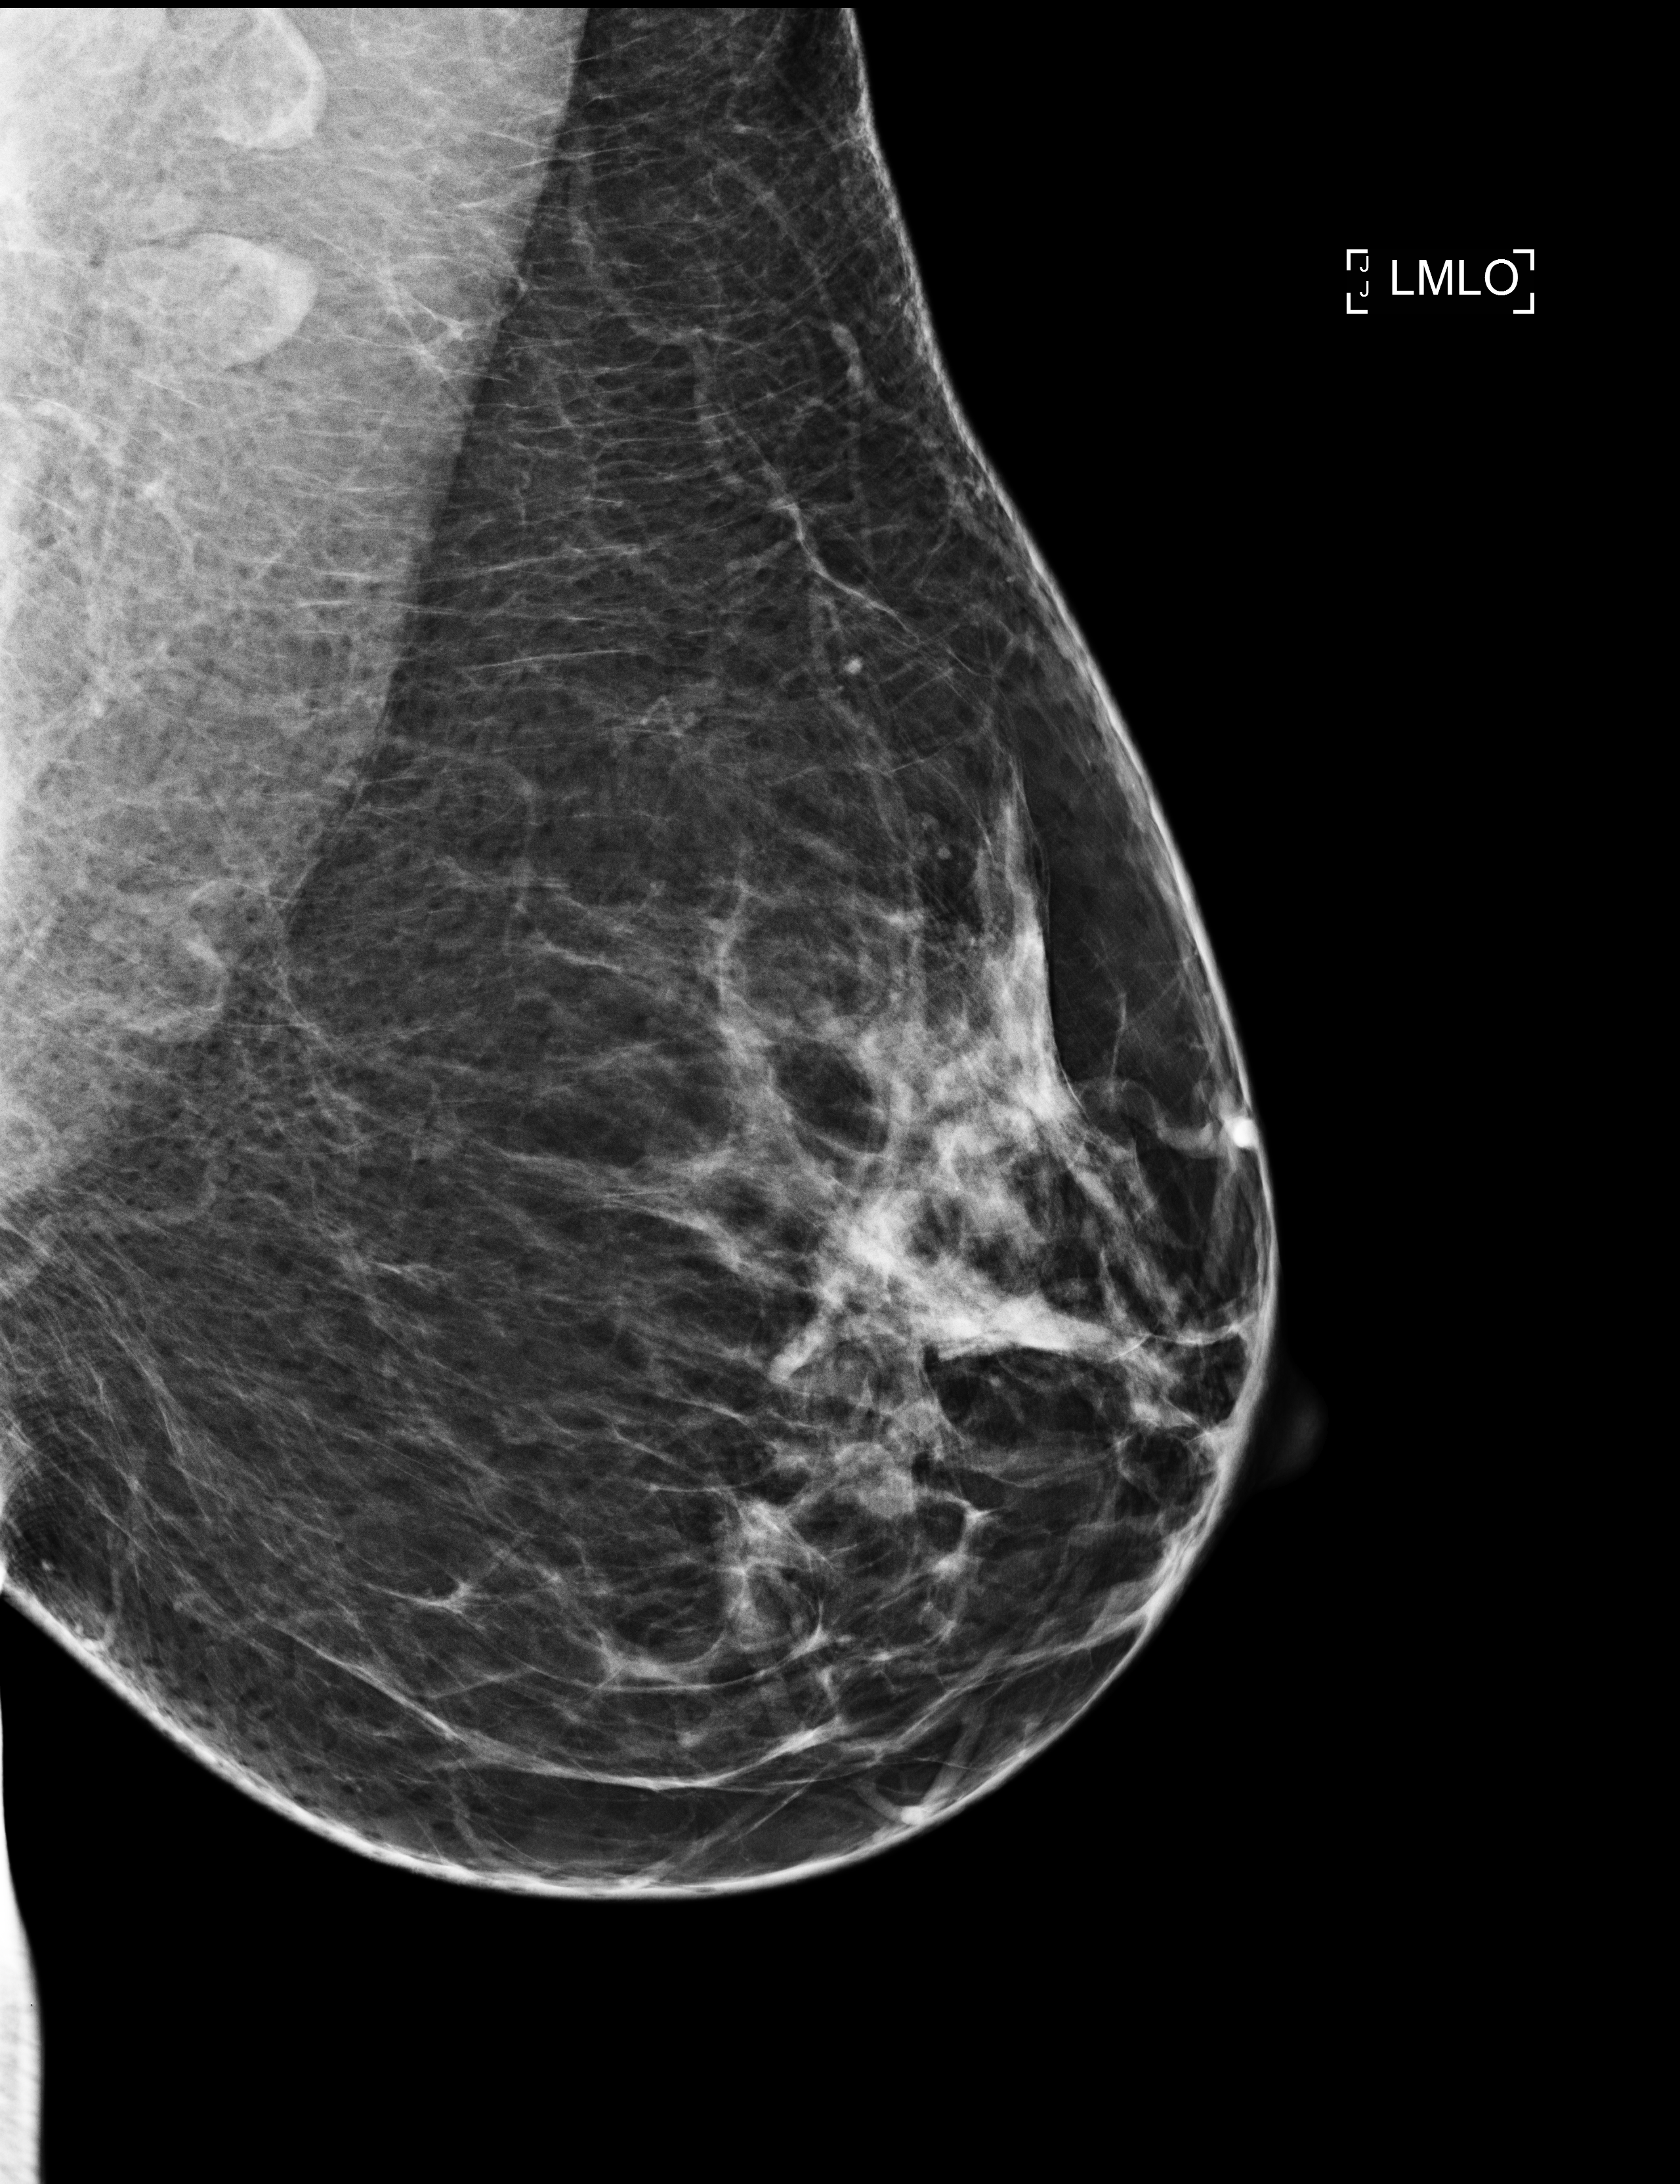
Screening examination, compressed breast thickness 73 mm. Female patient, age 41 years.
Image type: full-field digital mammogram. Breast: left. Projection: mediolateral oblique (MLO) view.